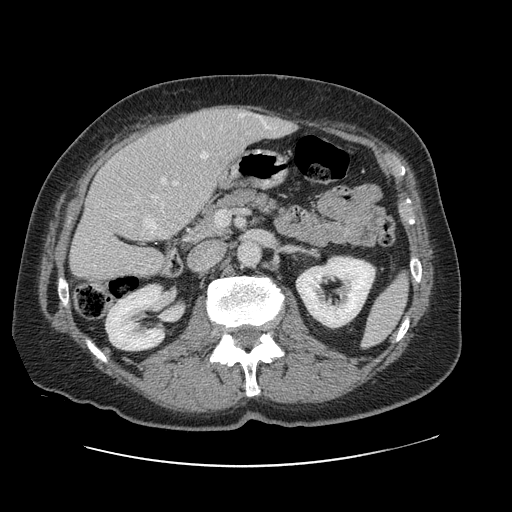
Contrast-enhanced abdominal CT, one axial slice. Slice 43 of 138 in the series (ordered by position). 120 kVp. Intravenous contrast given. Soft-tissue window (W 400 / L 40 HU). 512 × 512 image matrix, field of view 402 × 402 mm. Male patient, age 71 years. From the clinical record (not read from this slice): diagnosis: colorectal cancer liver metastases, imaged before liver resection.
Structures marked on this image (outlined manually by an expert reader):
- hepatic veins: box from (x=94, y=114) to (x=269, y=267) px
- liver: (x=71, y=106)–(x=294, y=281)
- planned liver remnant (the part of the liver to remain after resection): (x=71, y=136)–(x=194, y=281)
- portal vein (with intrahepatic branches): (x=161, y=179)–(x=166, y=183)